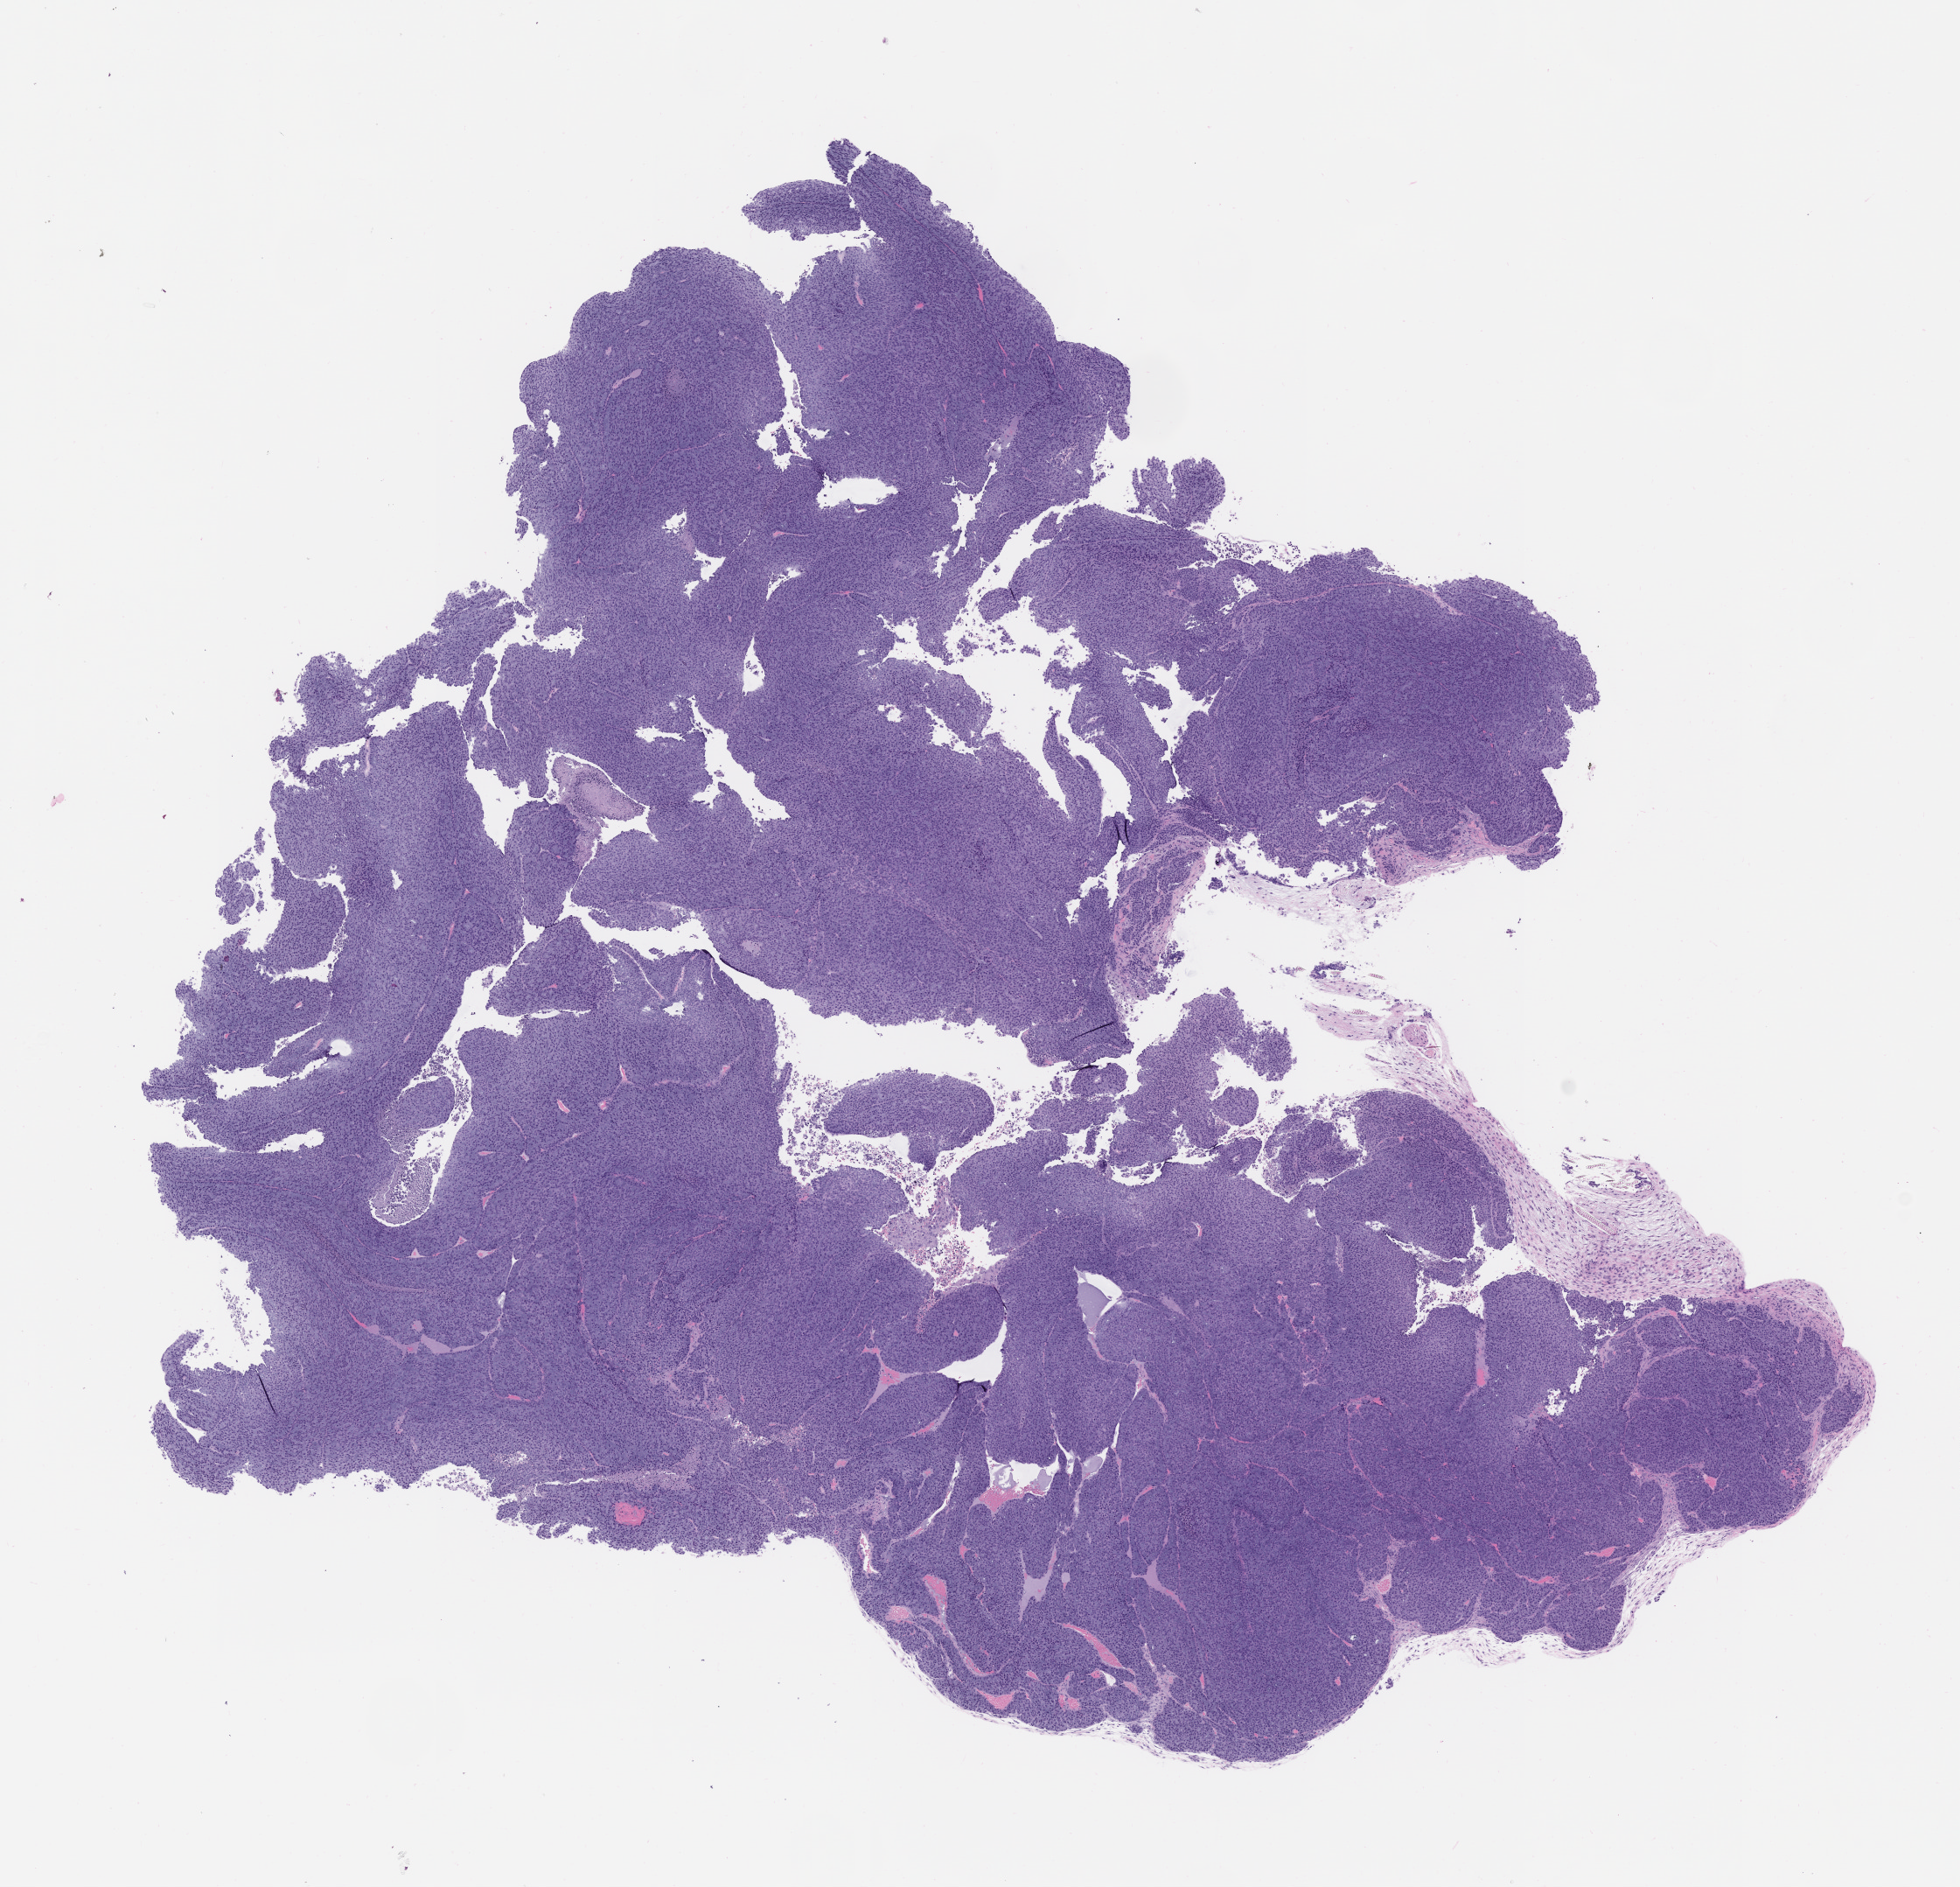
Whole-slide image, haematoxylin and eosin: patient-derived xenograft (human tumor grown in a mouse), passage 2, shown as a low-resolution overview of the whole scanned area (about 9.0 x 8.7 mm). Formalin-fixed paraffin-embedded section. Originating tumor site category: head and neck.
Originating patient diagnosis: Acinar Cell Carcinoma.